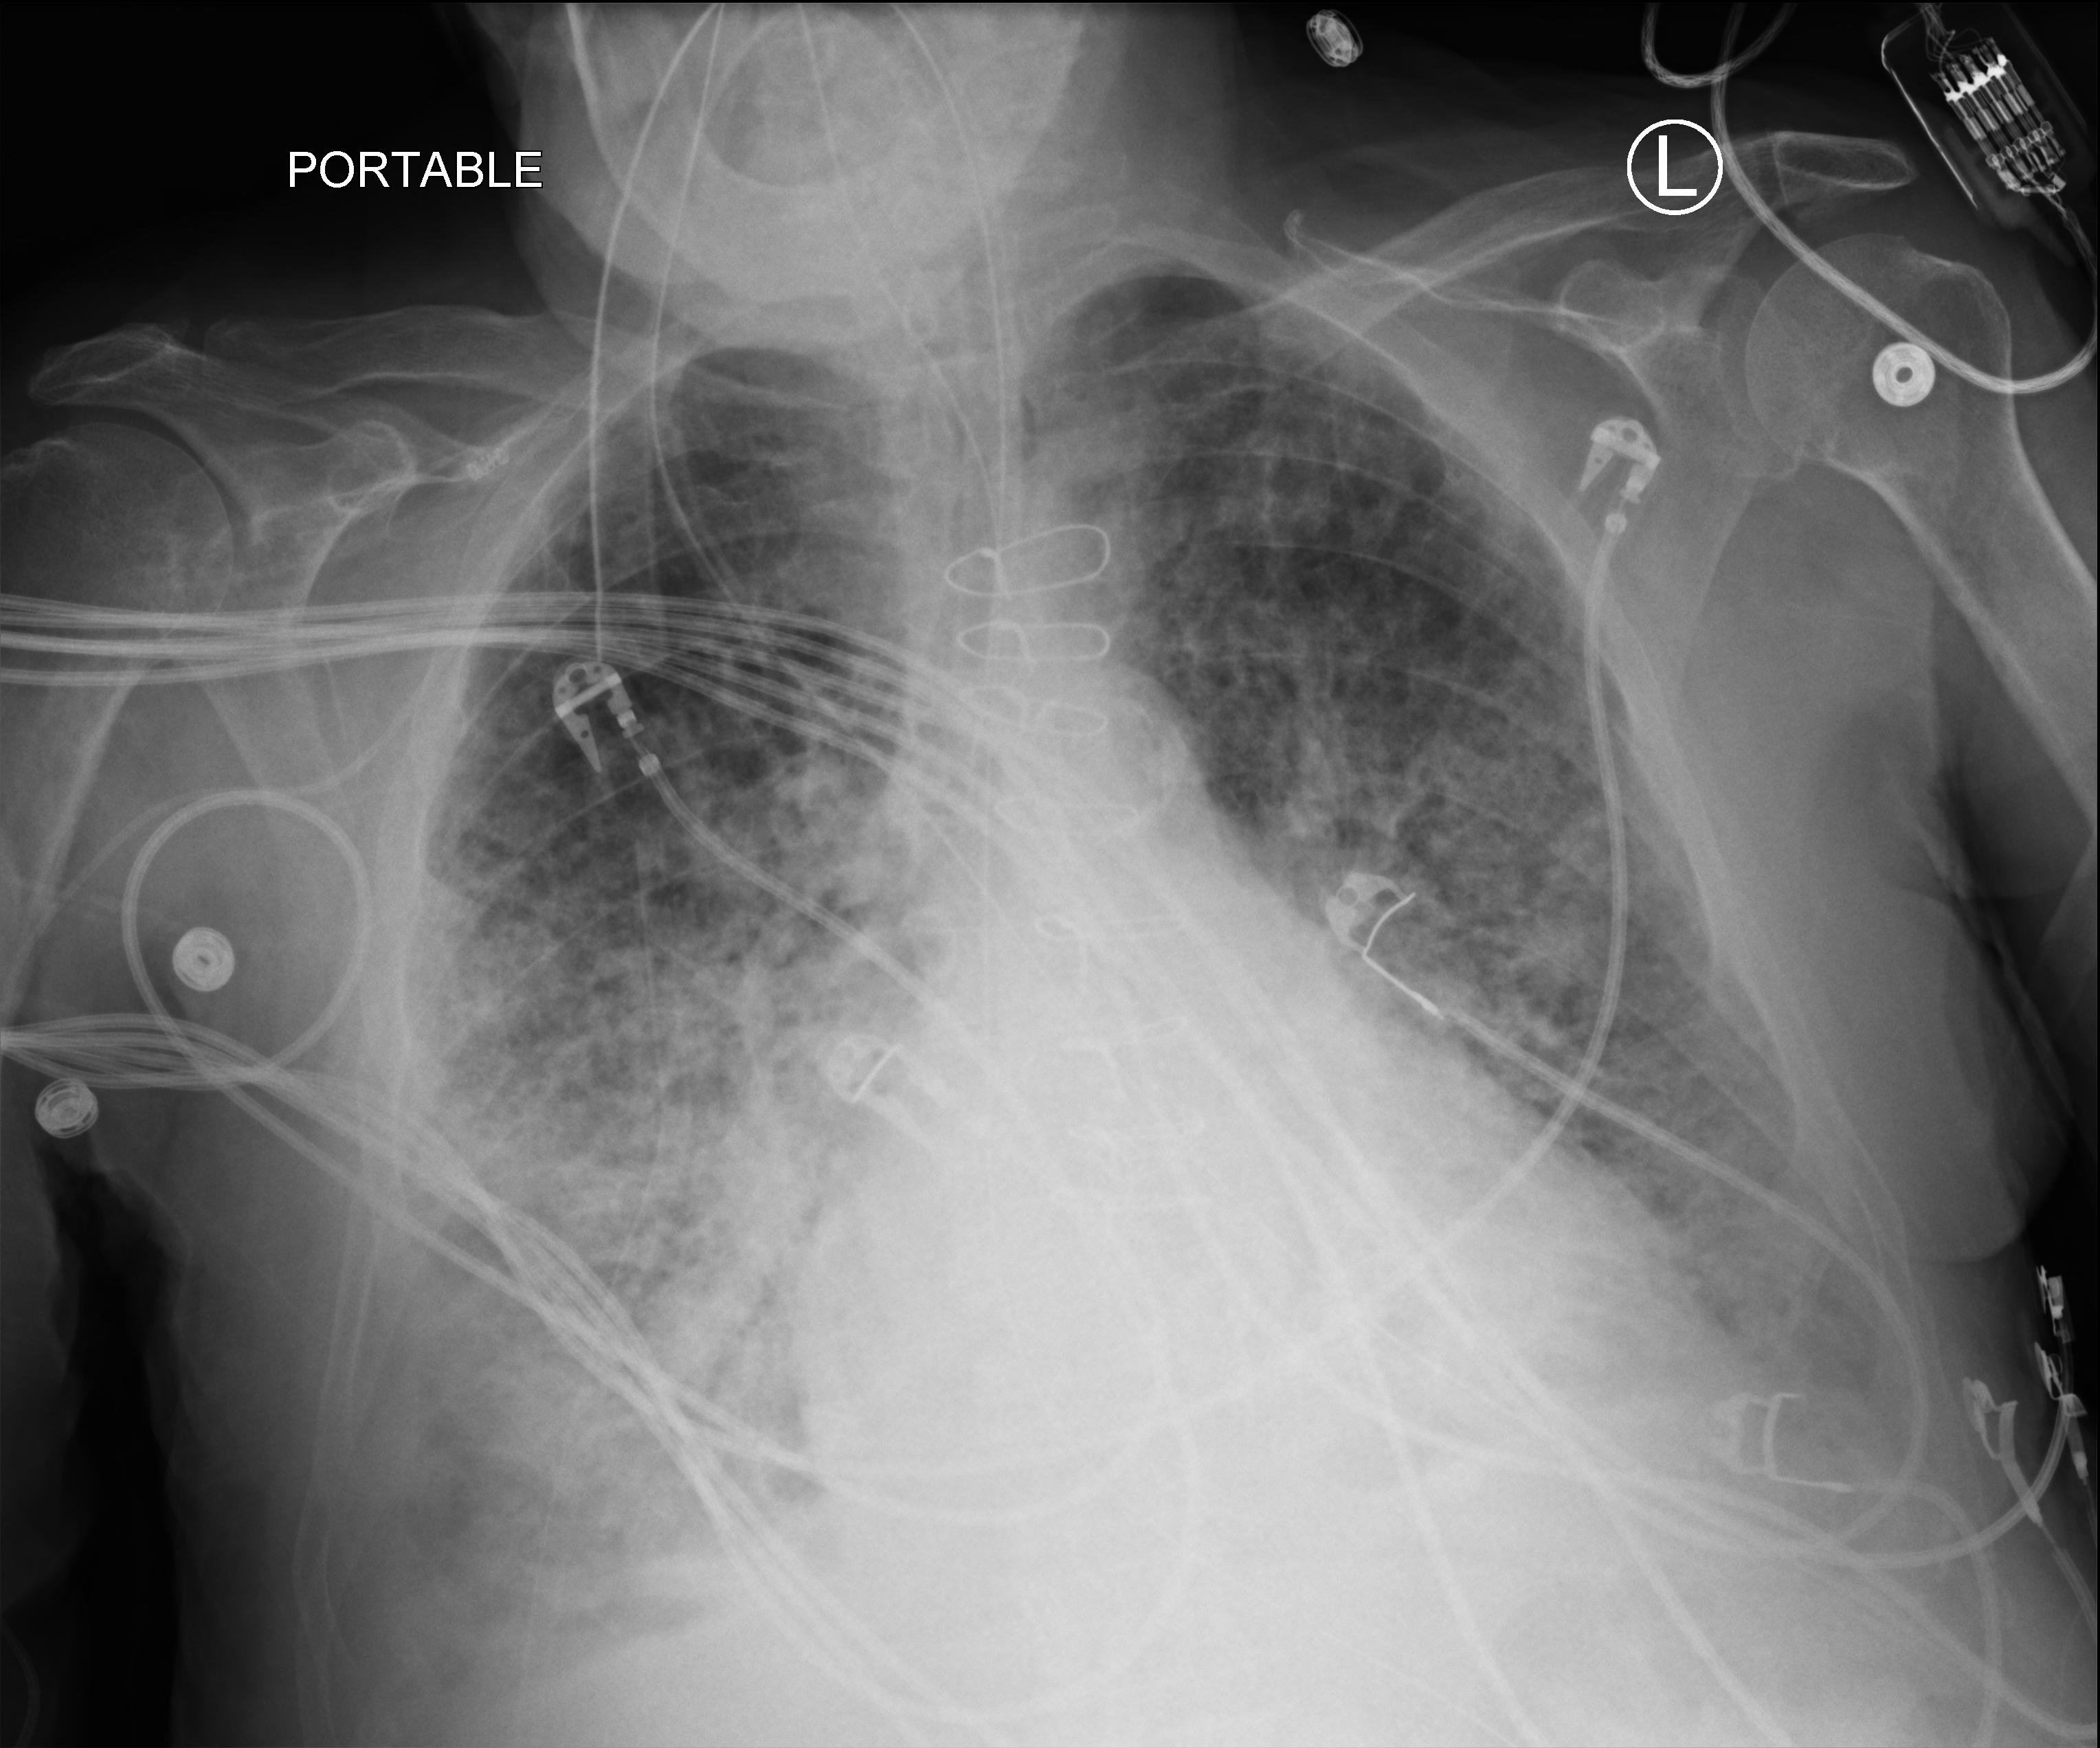
Chest X-ray (portable), anteroposterior (AP) projection. Patient hospitalised with COVID-19; male, aged 75–90 years.
From the hospital-stay record, not from the radiograph (when in the stay this image was taken is not recorded): admitted to intensive care during this hospital stay: yes; length of hospital stay: 40 days; mechanically ventilated during this hospital stay: yes.